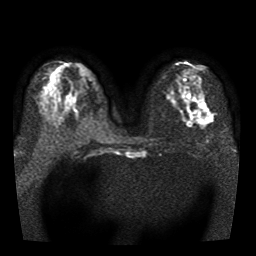
Breast MRI, one axial slice. Slice 18 of 41 in the series (ordered by position). Diffusion-weighted series; image 2 of 3 stored at this slice position (different b-values; order by instance number). 1.5 T. 5 mm slice thickness. 256 × 256 image matrix. Female patient.
Outlined on this slice (expert manual segmentation):
- tumour on diffusion-weighted imaging: box from (x=199, y=103) to (x=213, y=124) px